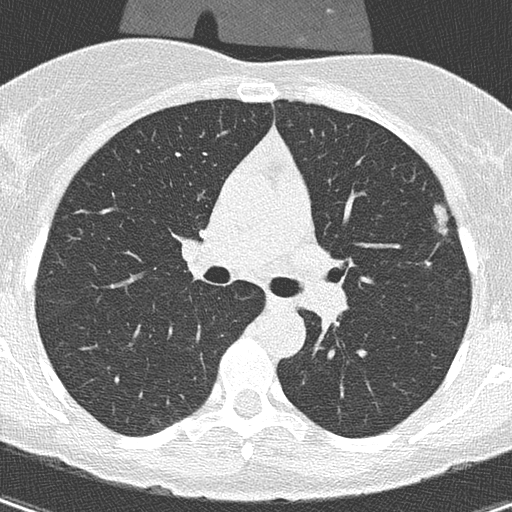
Low-dose screening chest CT, axial slice; baseline annual screen; lung window (W 1500 / L -600 HU); 120 kVp; slice 113 of 305 in the series. Female participant, aged 56 years at enrolment. Former smoker at enrolment.
Expert reader's lesion annotation, bounding box [x1, y1, x2, y2] px = [420, 194, 465, 249]. The exam's reader record, not a measurement of the box and not confirmed to be the same lesion: non-calcified nodule or mass ≥4 mm, left upper lobe, 110 × 106 mm, spiculated (stellate) margins, soft tissue attenuation. Participant outcome: lung cancer diagnosed 417 days after this screen — adenocarcinoma, NOS, left upper lobe, moderately differentiated (G2), stage IA (AJCC 6th edition), 11 mm at pathology.